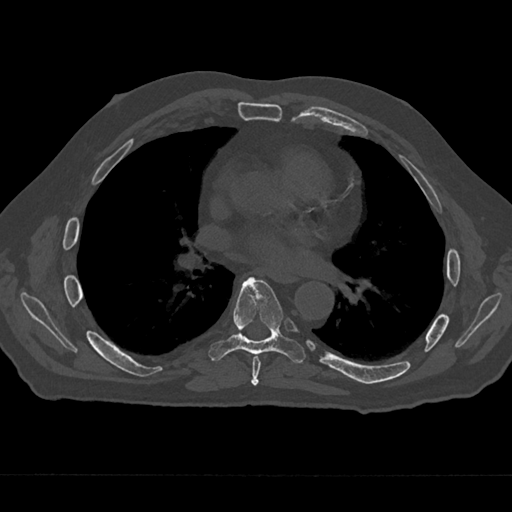
CT including the spine, one axial slice; slice 377 of 797 in the series (ordered by position); bone window (W 1800 / L 400 HU); 0.5 mm slice thickness; 512 × 512 image matrix, field of view 377 × 377 mm. Male patient, age 75 years. From the clinical record (not read from this slice): primary cancer: renal; vertebrae with lytic lesions (as recorded): T4.
Structures marked on this image (semi-automatic segmentation, software-assisted and operator-edited):
- T6 vertebra: box from (x=251, y=355) to (x=261, y=386) px
- T7 vertebra: (x=209, y=277)–(x=306, y=363)